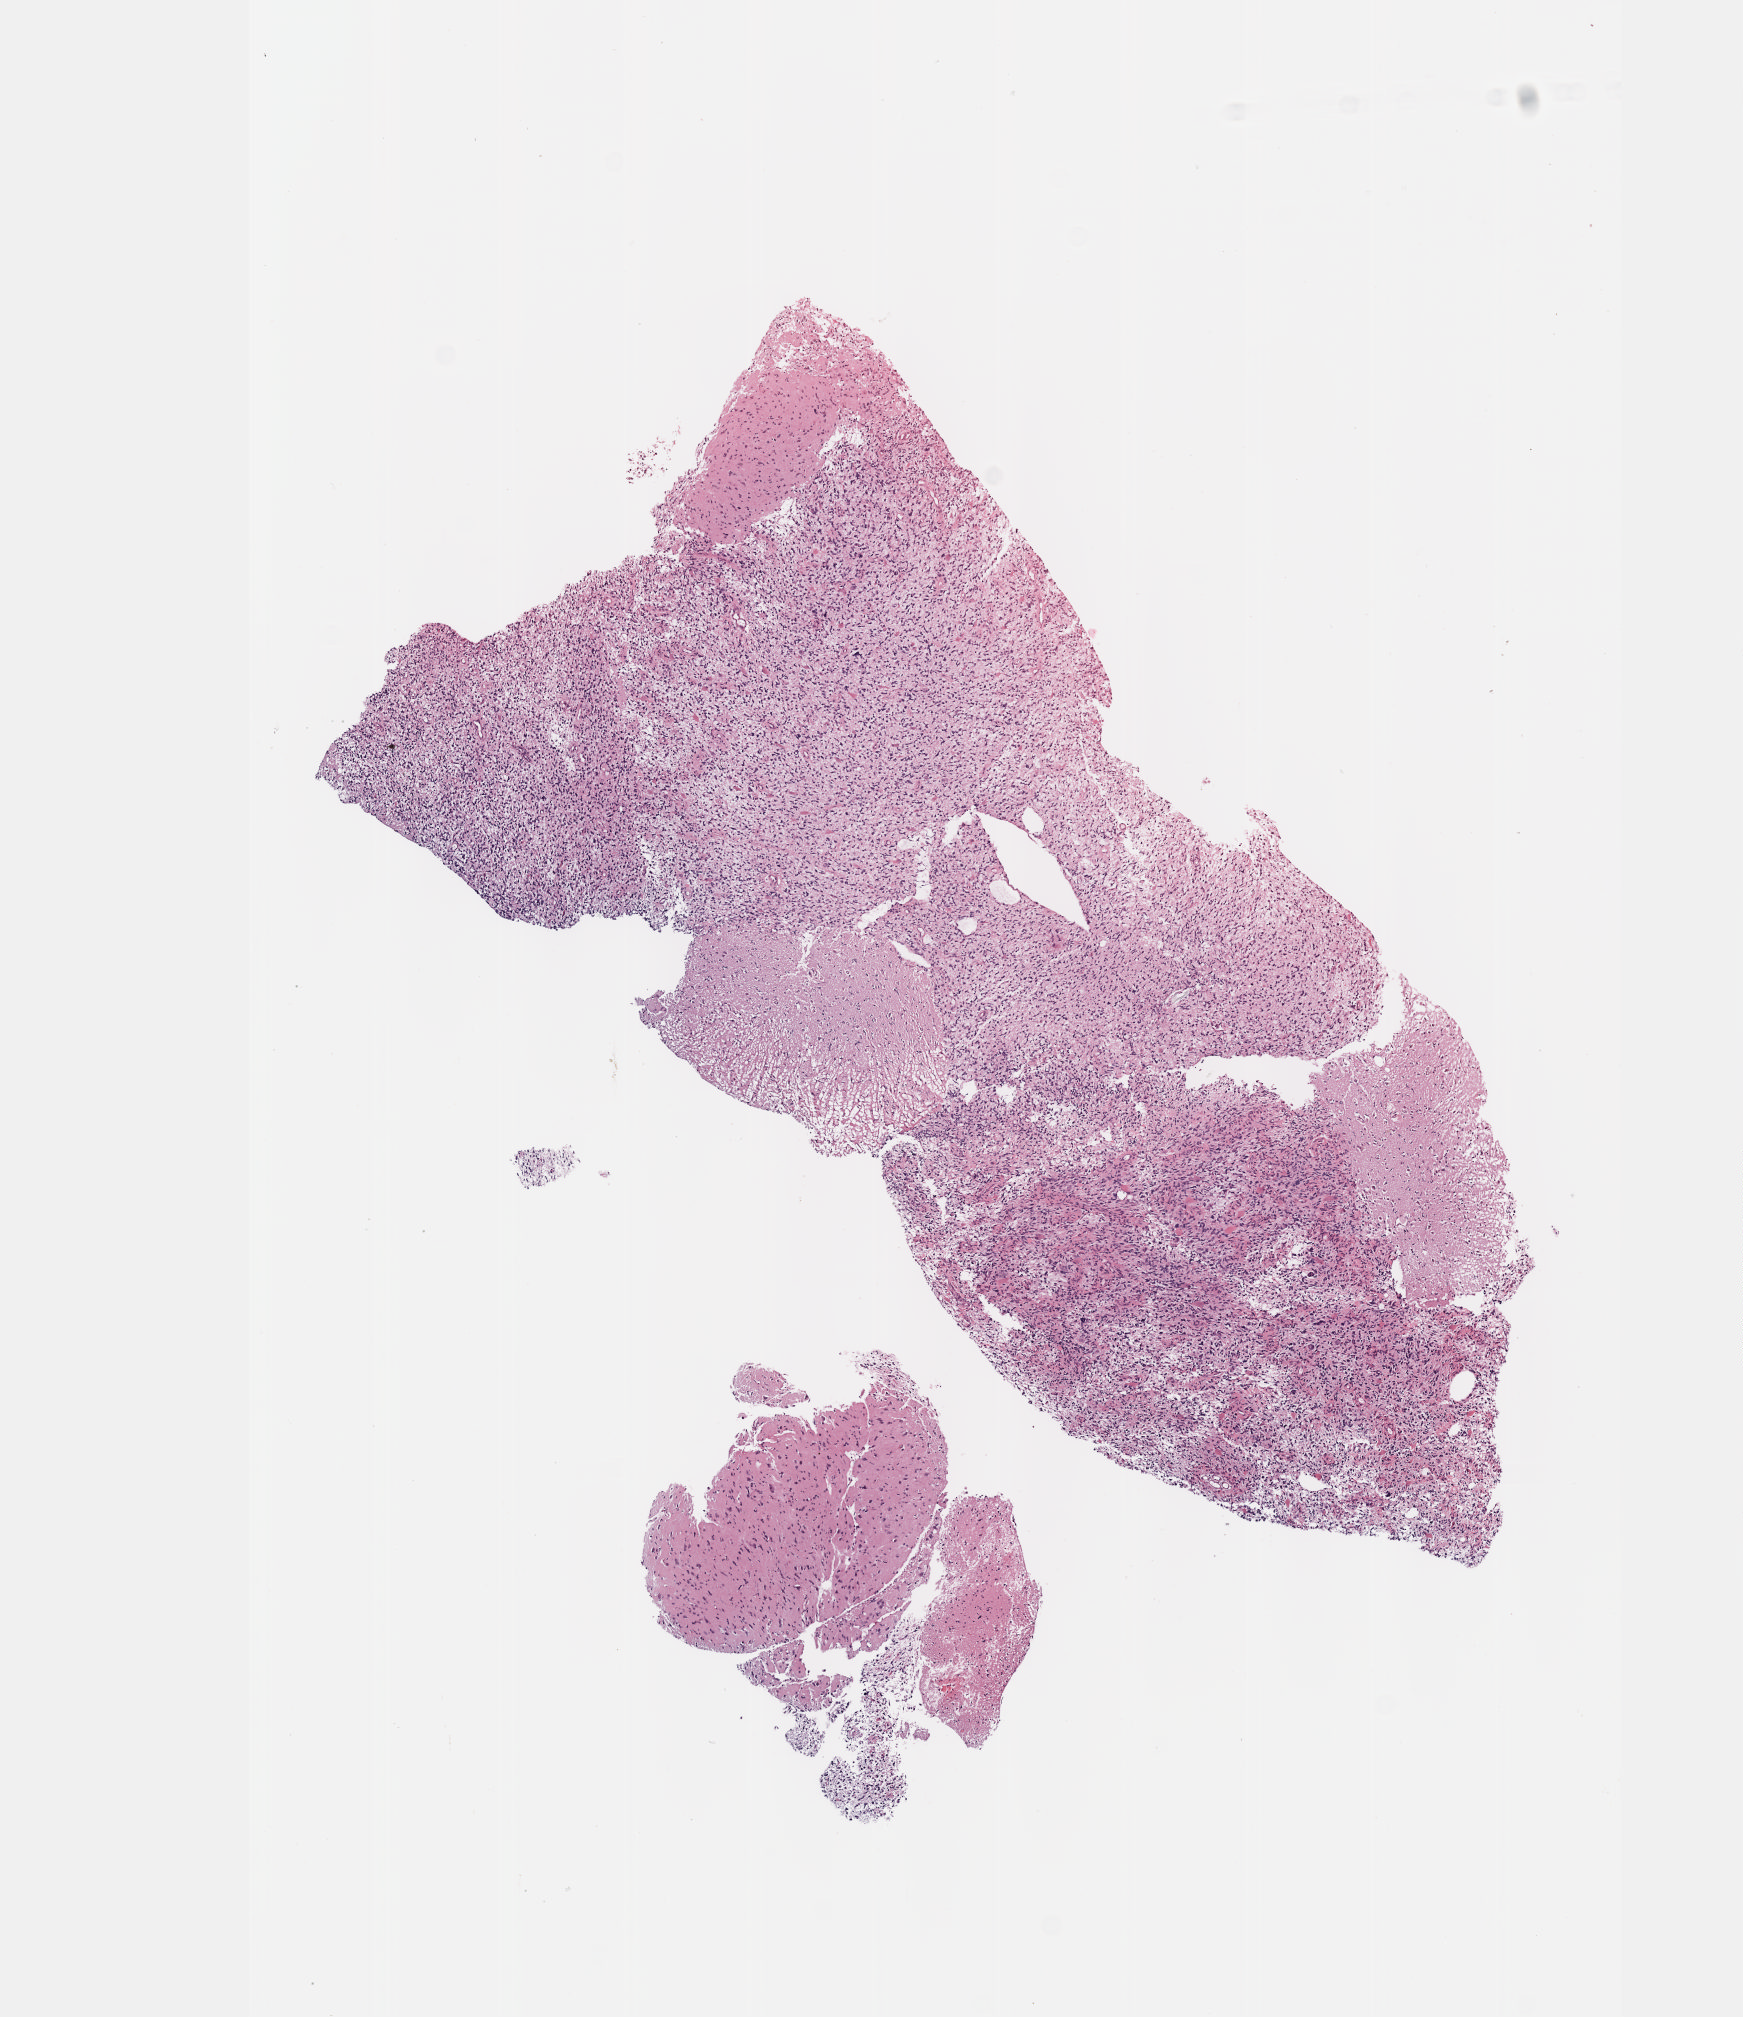
Digitized H&E tissue section (whole slide), whole scanned area (about 7.0 x 8.1 mm, slide scanned at 40x) shown as a low-resolution overview. Formalin-fixed paraffin-embedded (FFPE) diagnostic section. Brain, primary tumour sample. Patient: female, age at initial diagnosis 58 years. Histologic grade: G3 (poorly differentiated).
* diagnosis: Astrocytoma, anaplastic (cerebrum)
* laterality: left